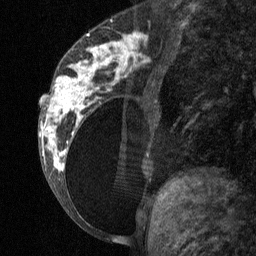
Breast MRI (dynamic contrast-enhanced), one sagittal slice; position 28 of 64 along the scan axis; dynamic contrast-enhanced study with each time point stored as its own series, time point 2 of 3 at this slice position (early post-contrast, ordered by acquisition time); 1.5 T; TE 4.8 ms, TR 27 ms; 2 mm slice thickness; 256 × 256 image matrix, field of view 180 × 180 mm. Female patient, age 34 years. Case-level facts recorded for this patient, not image findings: setting: breast cancer imaged before/during neoadjuvant chemotherapy; receptor status: HR-positive, HER2-negative.
Outlined on this slice (semi-automatically segmented with operator editing):
- analysis volume of interest (the breast-tissue region the enhancement analysis was run in; not a lesion): box from (x=41, y=23) to (x=157, y=197) px
- tumour enhancement mask (voxels above the 90 % enhancement threshold inside the analysis volume of interest): (x=41, y=33)–(x=144, y=171)